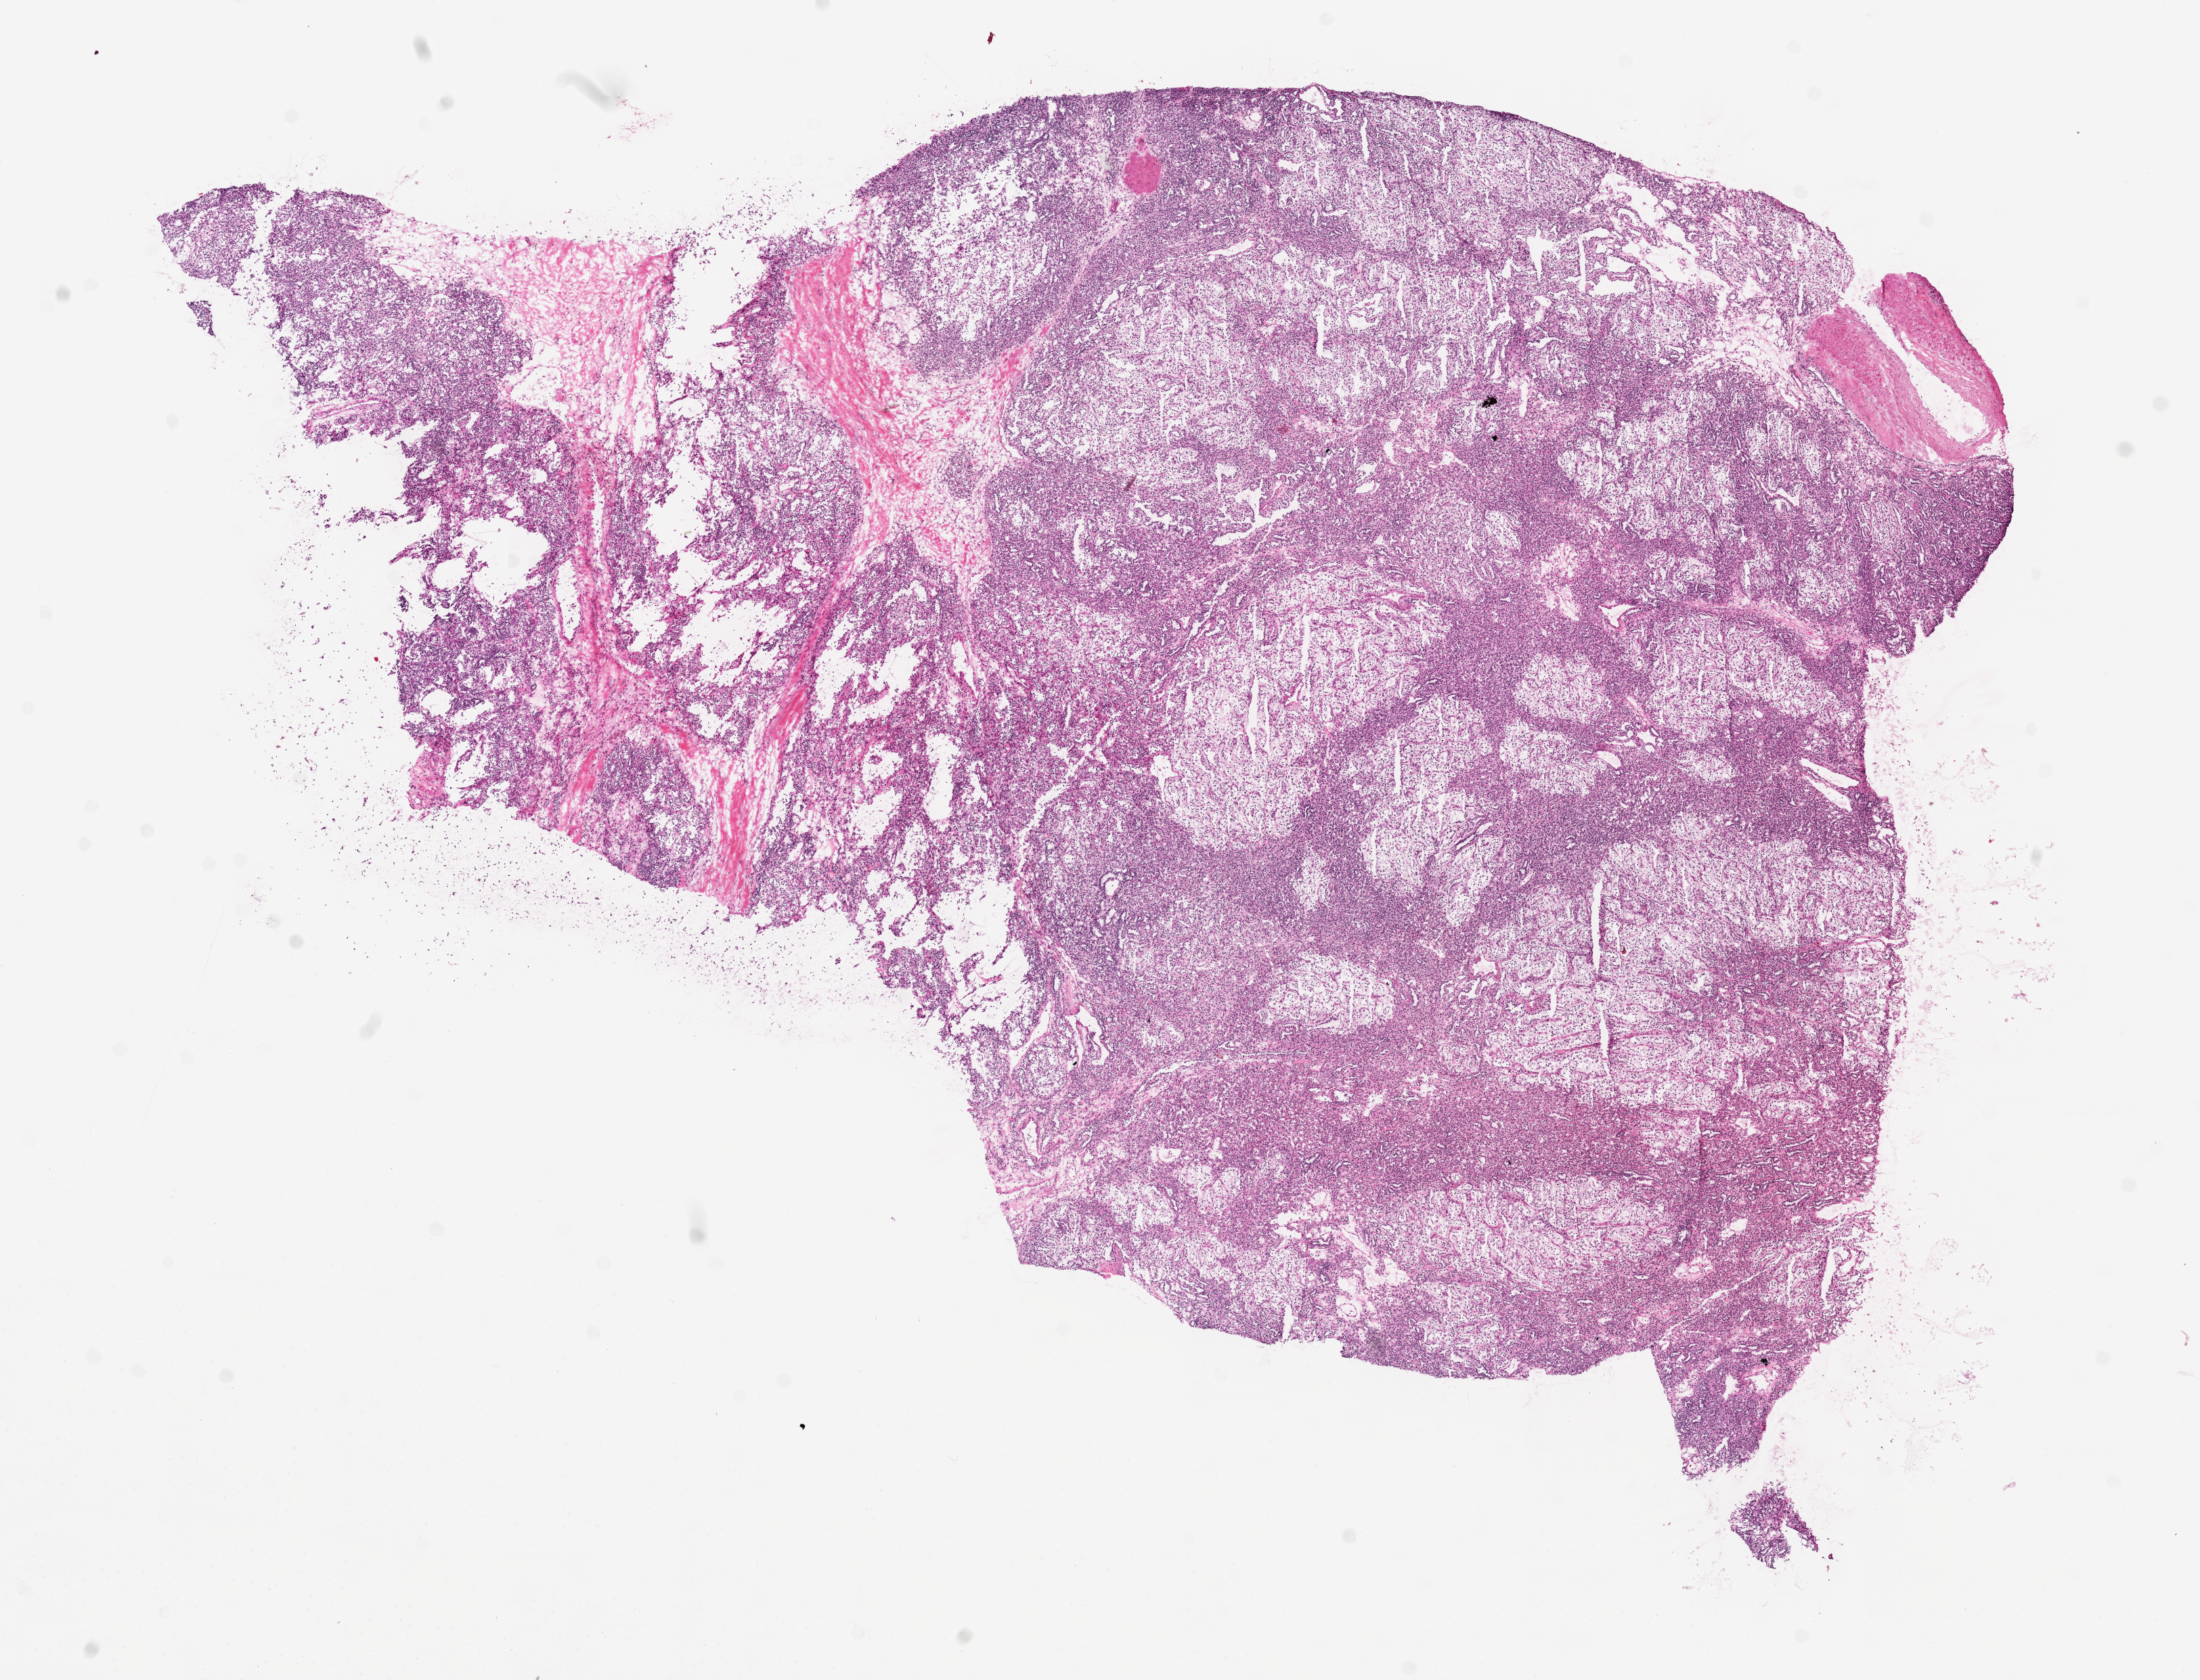
Hematoxylin and eosin (H&E) stained whole-slide image, low-resolution overview of the scanned area, about 13.0 x 10.0 mm, frozen section from the top of the tissue portion, sample: primary tumour, kidney. Male patient; age at initial diagnosis 62 years. Histologic grade: G2 (moderately differentiated). Slide review estimates, as recorded: tumour cells 95%, tumour nuclei 95%, normal cells 0%, stromal cells 5%, necrosis 0%. Inflammatory infiltration, as recorded: lymphocyte infiltration 1%, monocyte infiltration 0%, neutrophil infiltration 1%.
TNM: T1 N0 M0. AJCC pathologic stage: I (7th edition). Histologic diagnosis: Clear cell adenocarcinoma, NOS. Laterality: right.